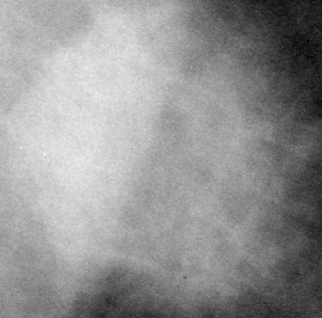
Crop from a digitized film mammogram around one marked abnormality; left breast; MLO view.
Finding: mass, shape round, margins ill defined; BI-RADS assessment category 4; pathology (as recorded): malignant.